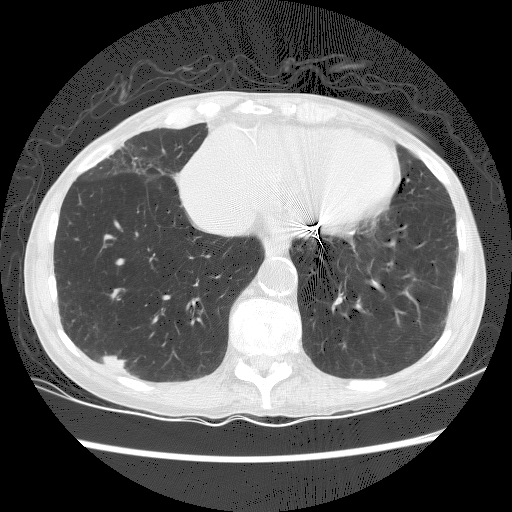
Low-dose screening chest CT, one axial slice. Slice 58 of 156 in the series (ordered by position). Reconstruction kernel BONE. Lung window (W 1500 / L -600 HU). 512 × 512 image matrix.
Annotated regions visible in this slice (outlined manually by an expert reader):
- lesion 1 (tumor, lower lobe of right lung): bounding box <103,352,136,372> (left, top, right, bottom; pixels)